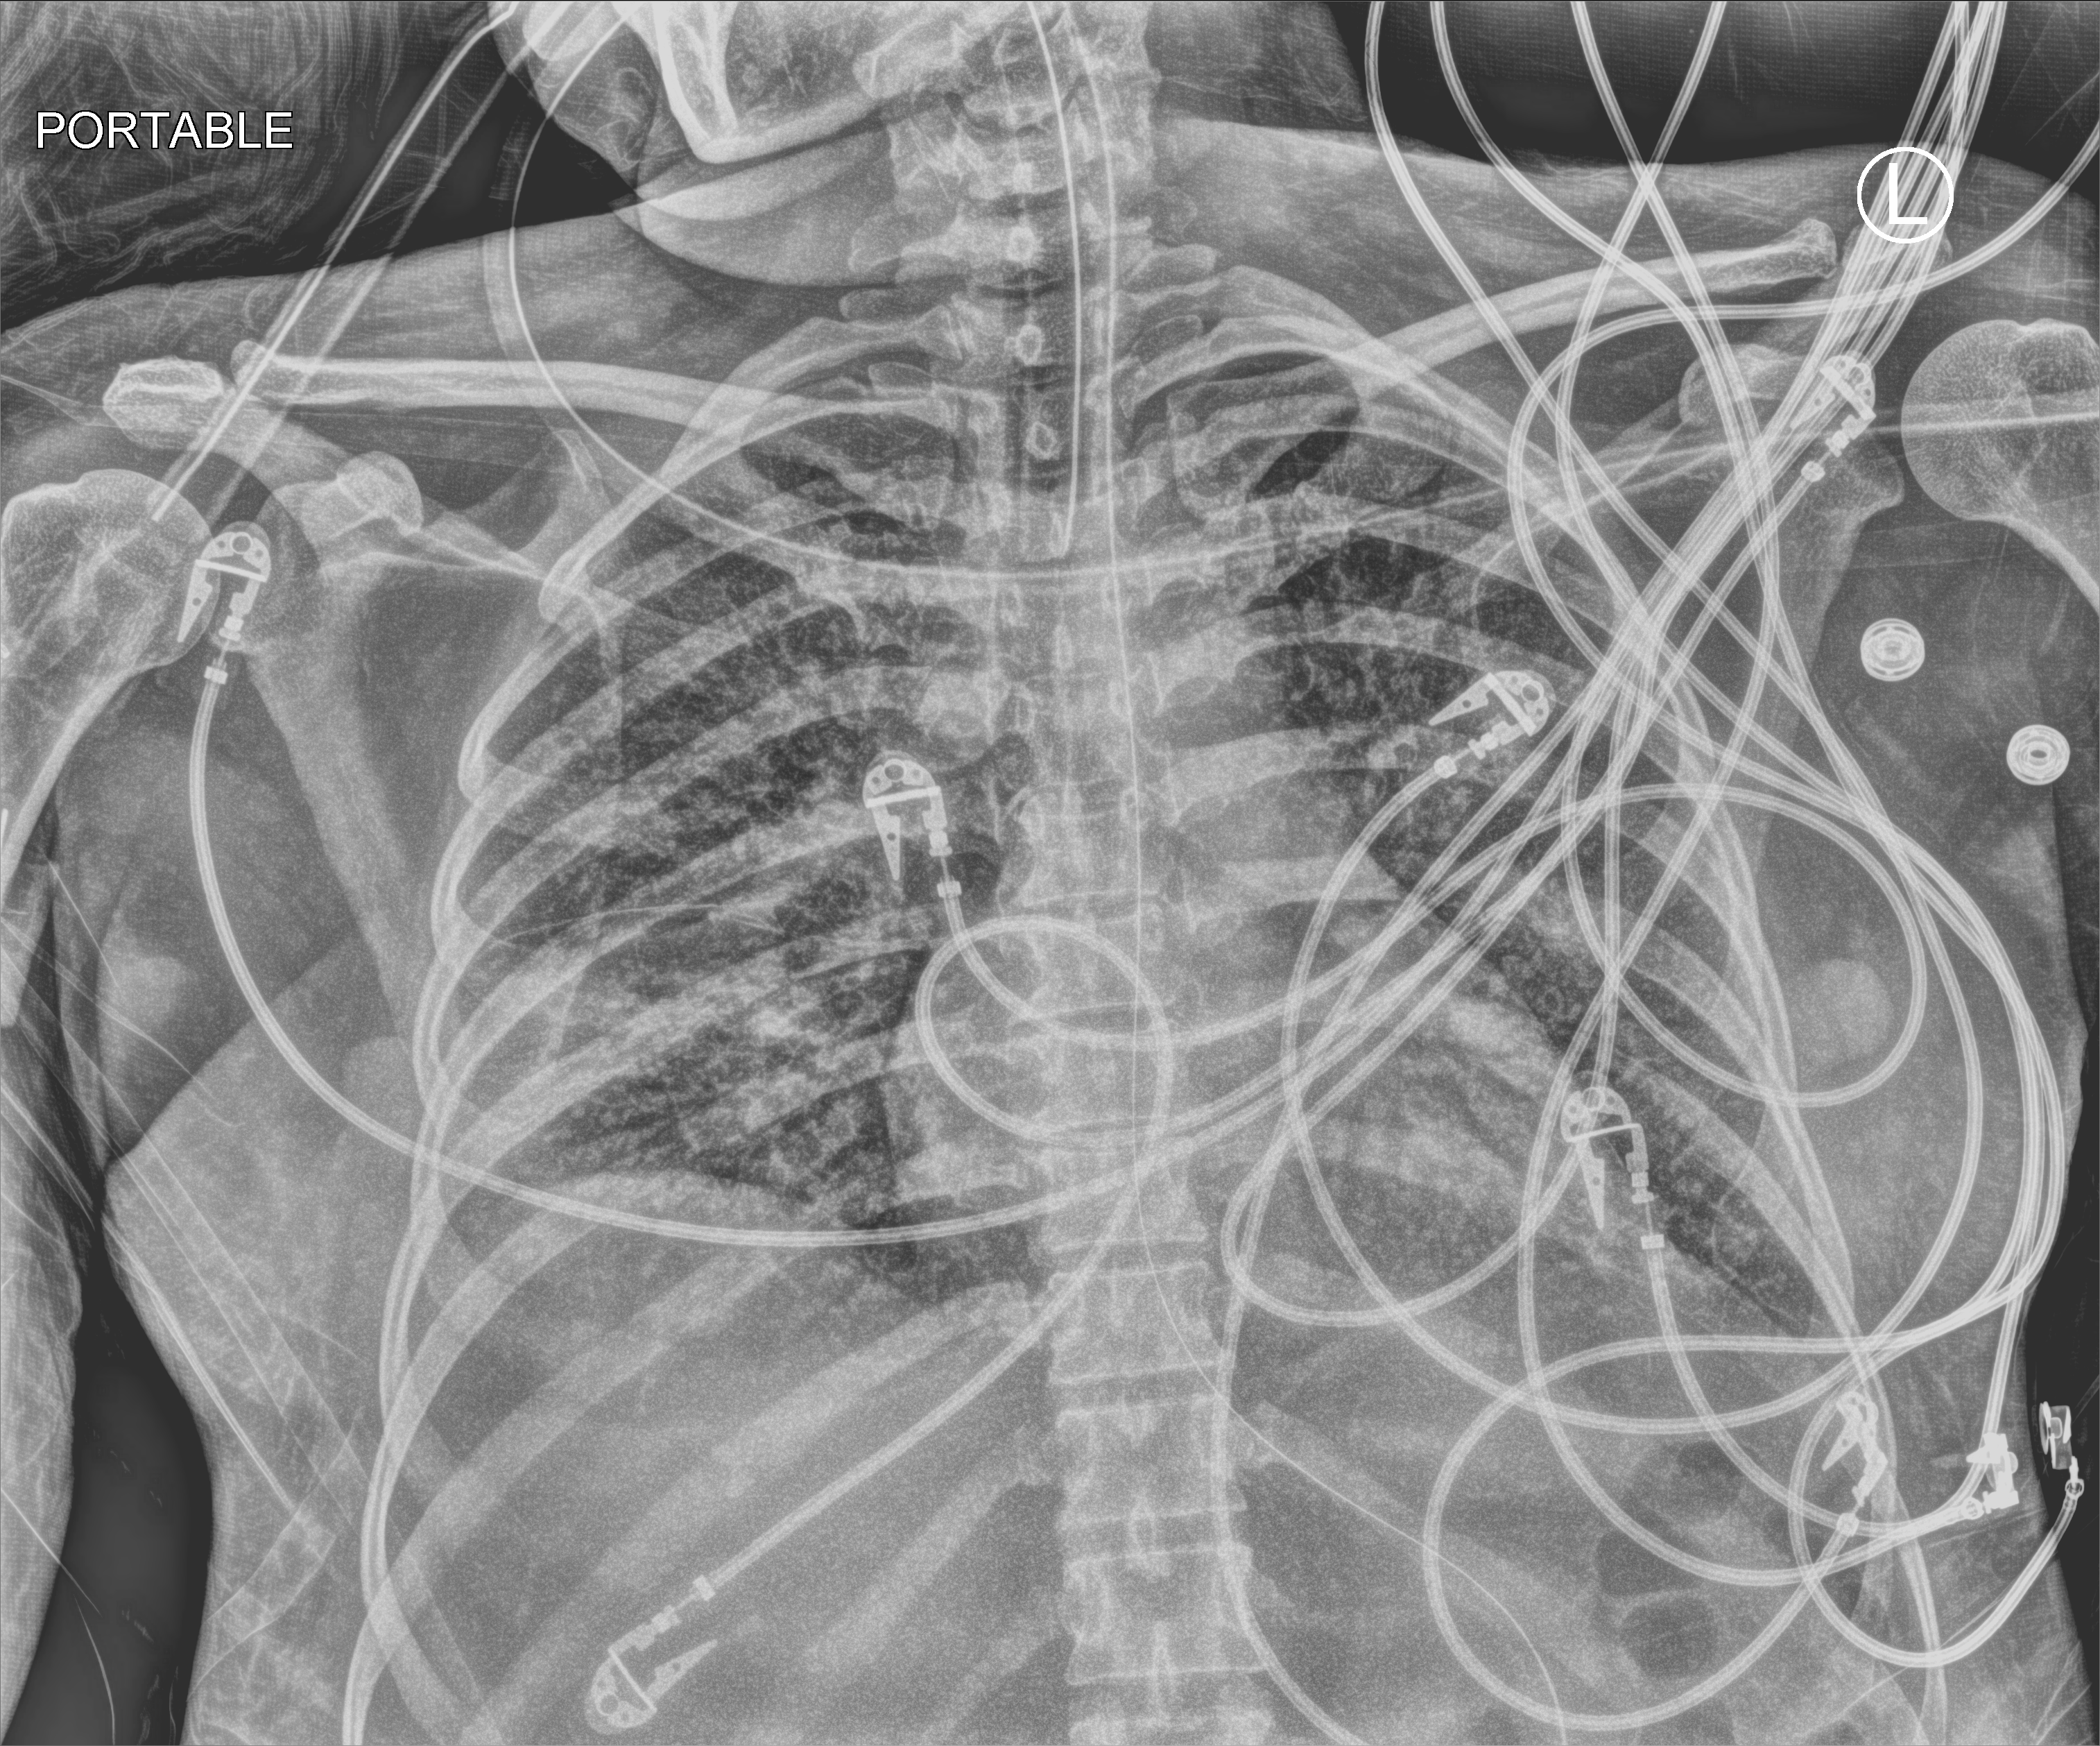
Portable chest radiograph; anteroposterior (AP) projection. Female patient hospitalised with COVID-19, age 18–59 years.
Admission-level facts for this patient (not findings on this image; timing relative to this image not recorded):
- mechanically ventilated during this hospital stay: yes
- admitted to intensive care during this hospital stay: yes